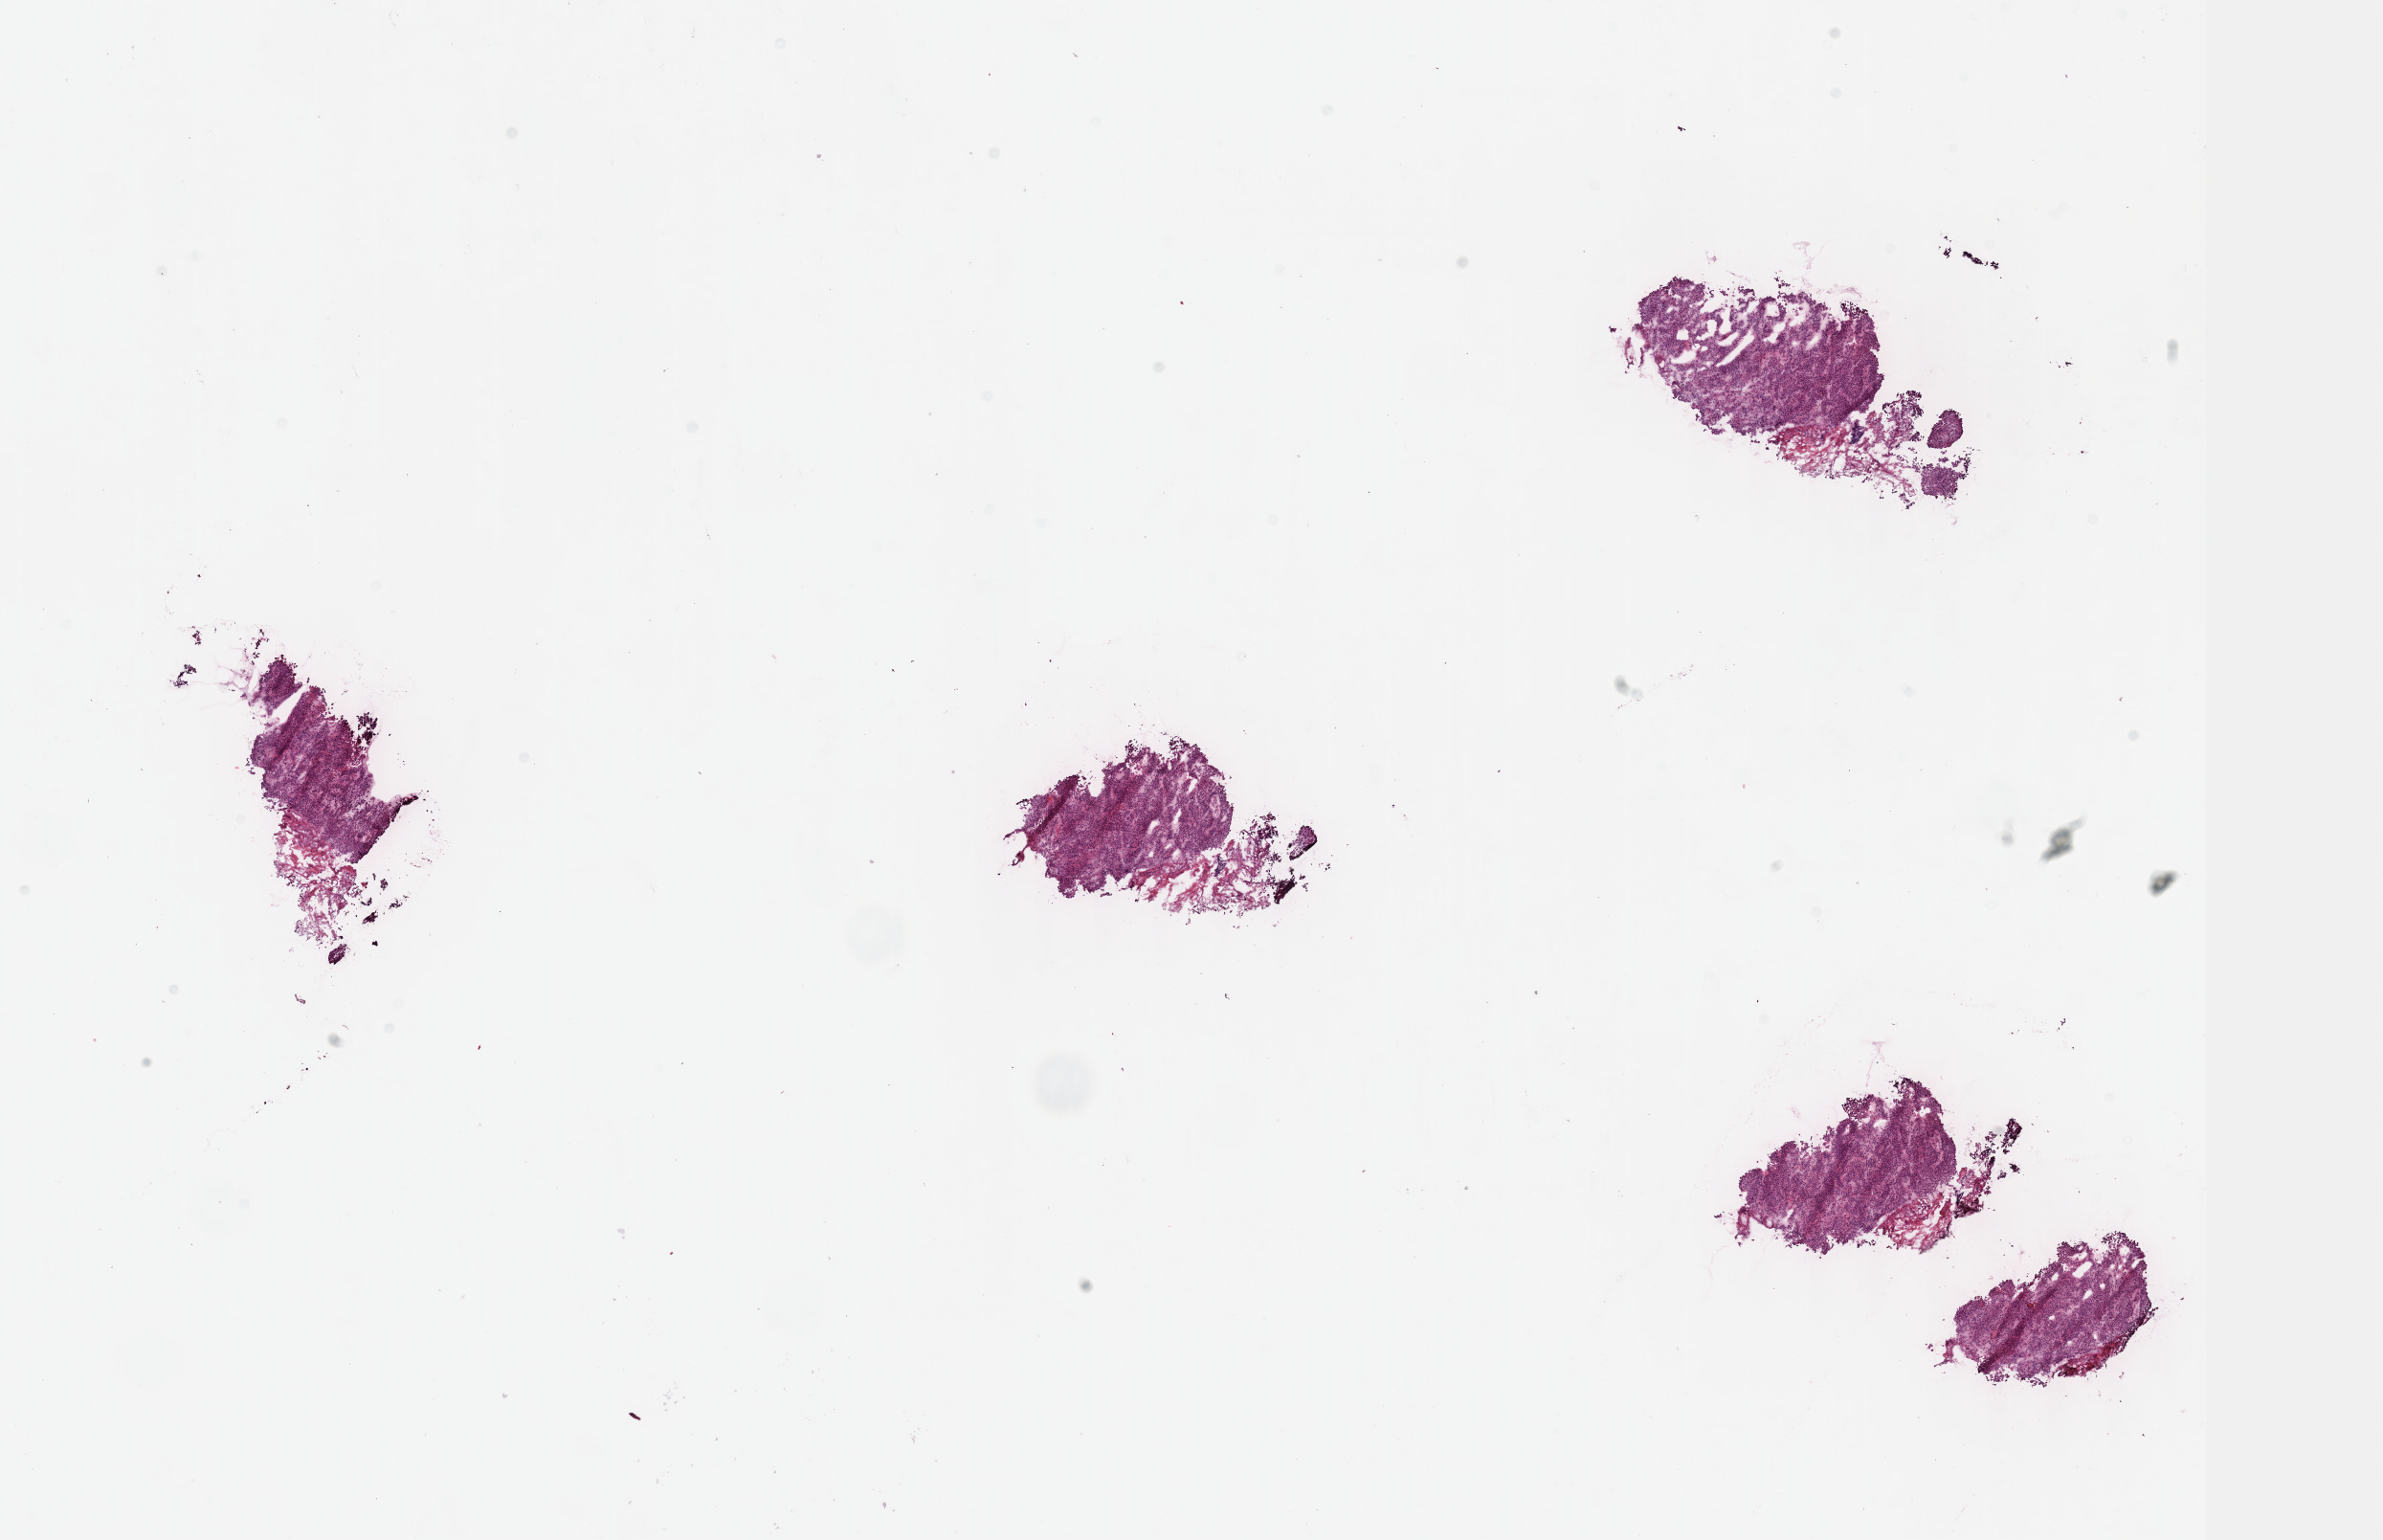
Whole-slide histology image, H&E, low-resolution overview of the scanned area, about 20.1 x 13.0 mm (from a 40x scan); frozen section from the top of the tissue portion; bladder, primary tumour sample. Patient: male, age at initial diagnosis 61 years. Histologic grade: high grade. Slide review estimates, as recorded: tumour cells 70%, tumour nuclei 95%, normal cells 0%, stromal cells 15%, necrosis 15%. Inflammatory infiltration, as recorded: lymphocyte infiltration 3%, monocyte infiltration 0%, neutrophil infiltration 1%.
• diagnosis: Transitional cell carcinoma
• AJCC pathologic stage: II (6th edition)